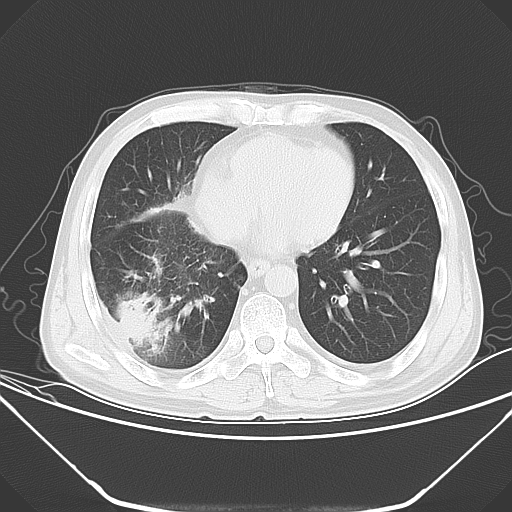
Chest CT, one axial slice; position 17 of 52 along the scan axis; 120 kVp; lung window (W 1500 / L -600 HU); 512 × 512 image matrix, field of view 379 × 379 mm. Male patient, age 54 years. Case-level facts recorded for this patient, not image findings: clinical TNM (as recorded): T2 N1 M0.
Outlined on this slice (rectangle marked by the reading radiologist):
- lung tumour (recorded histology: adenocarcinoma): bounding box <117,293,174,355> (left, top, right, bottom; pixels)